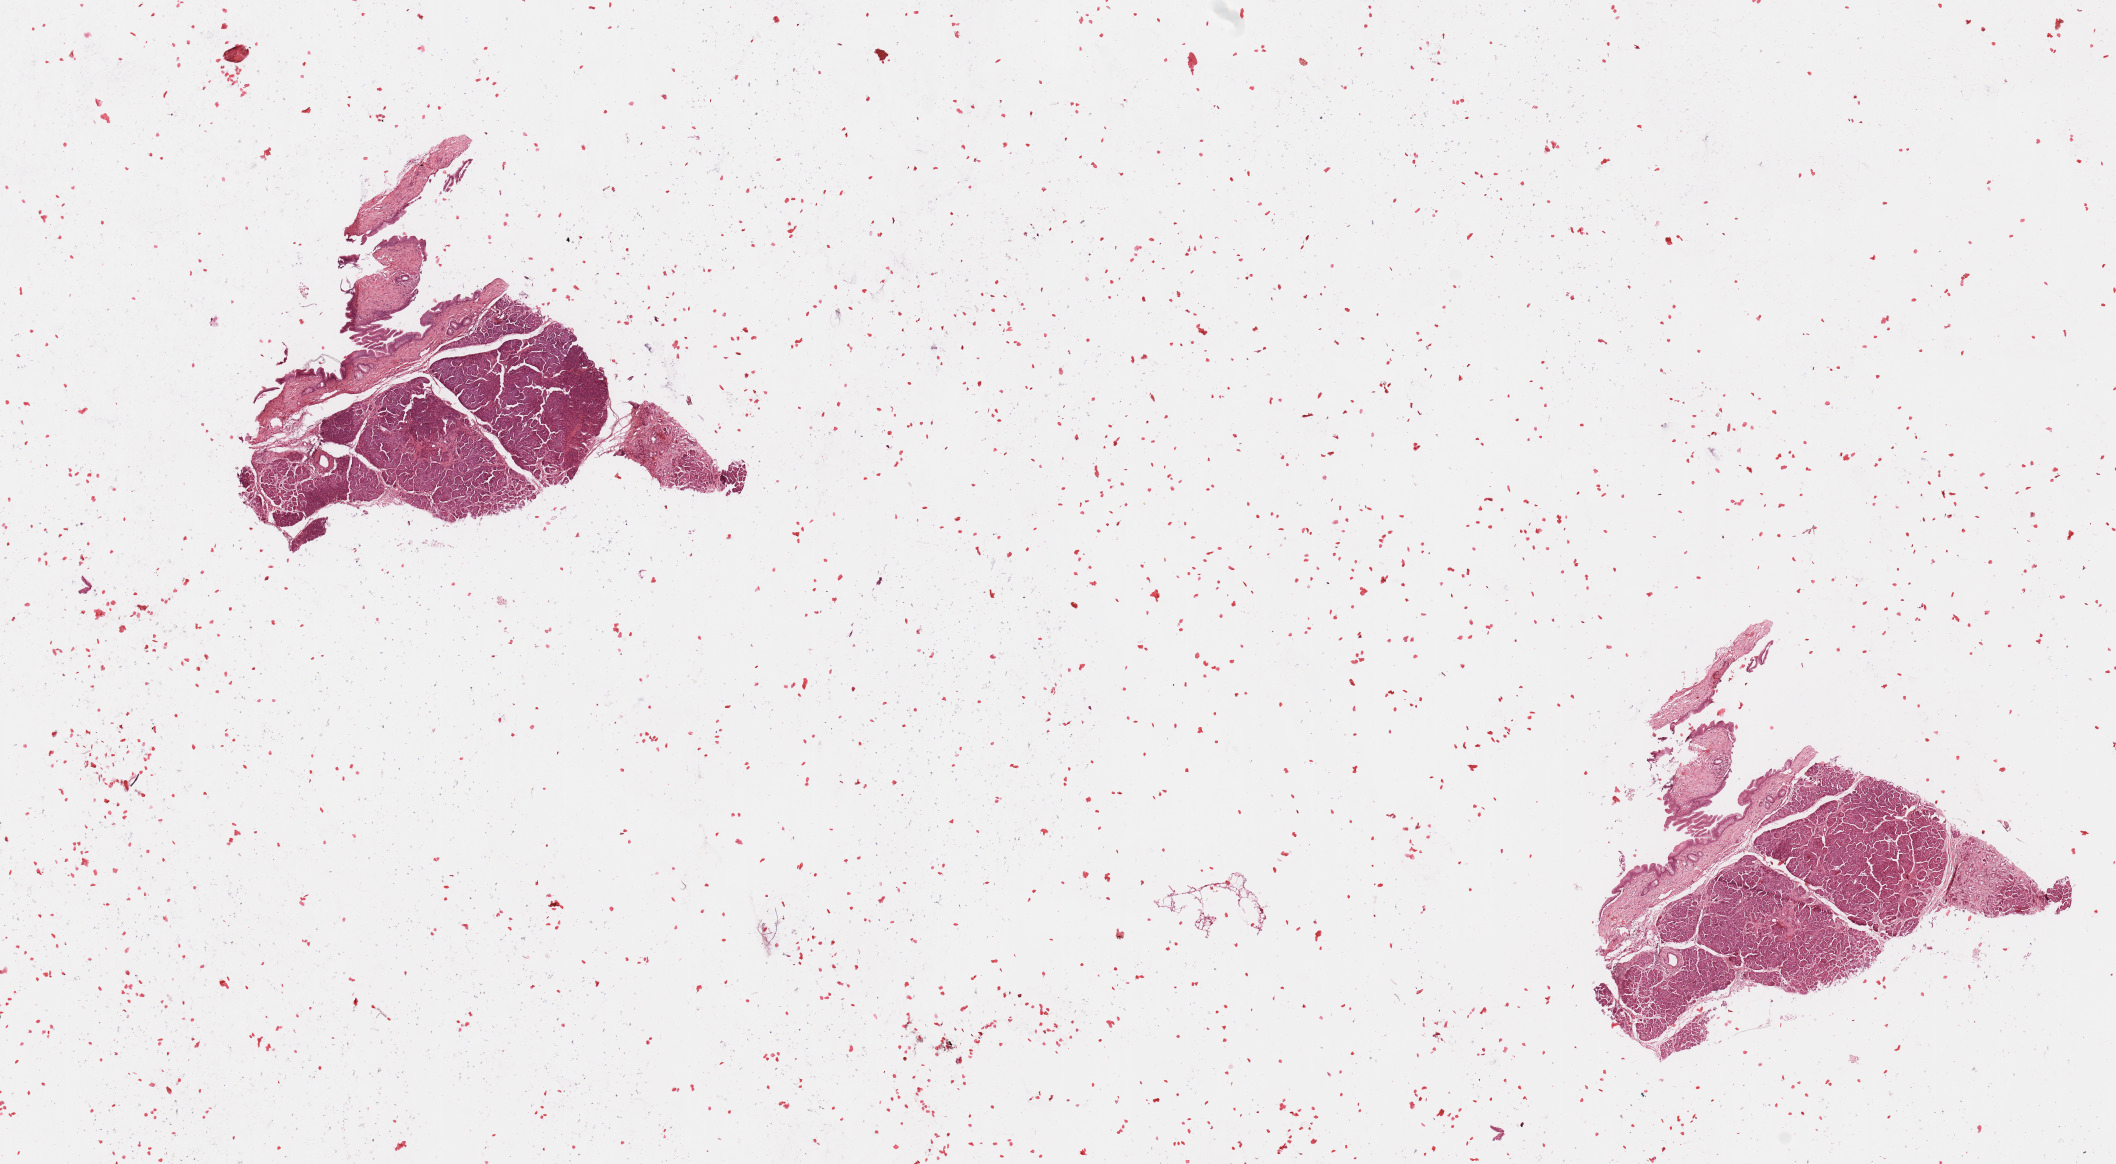
Whole-slide histology image, H&E, low-resolution overview of the scanned area, about 16.7 x 9.2 mm (slide scanned at 20x), normal (non-tumour) tissue sample, sampled site: pancreas. 63-year-old male patient.
This section: normal (non-tumour) tissue from the same patient. Patient diagnosis: Infiltrating duct carcinoma, NOS.